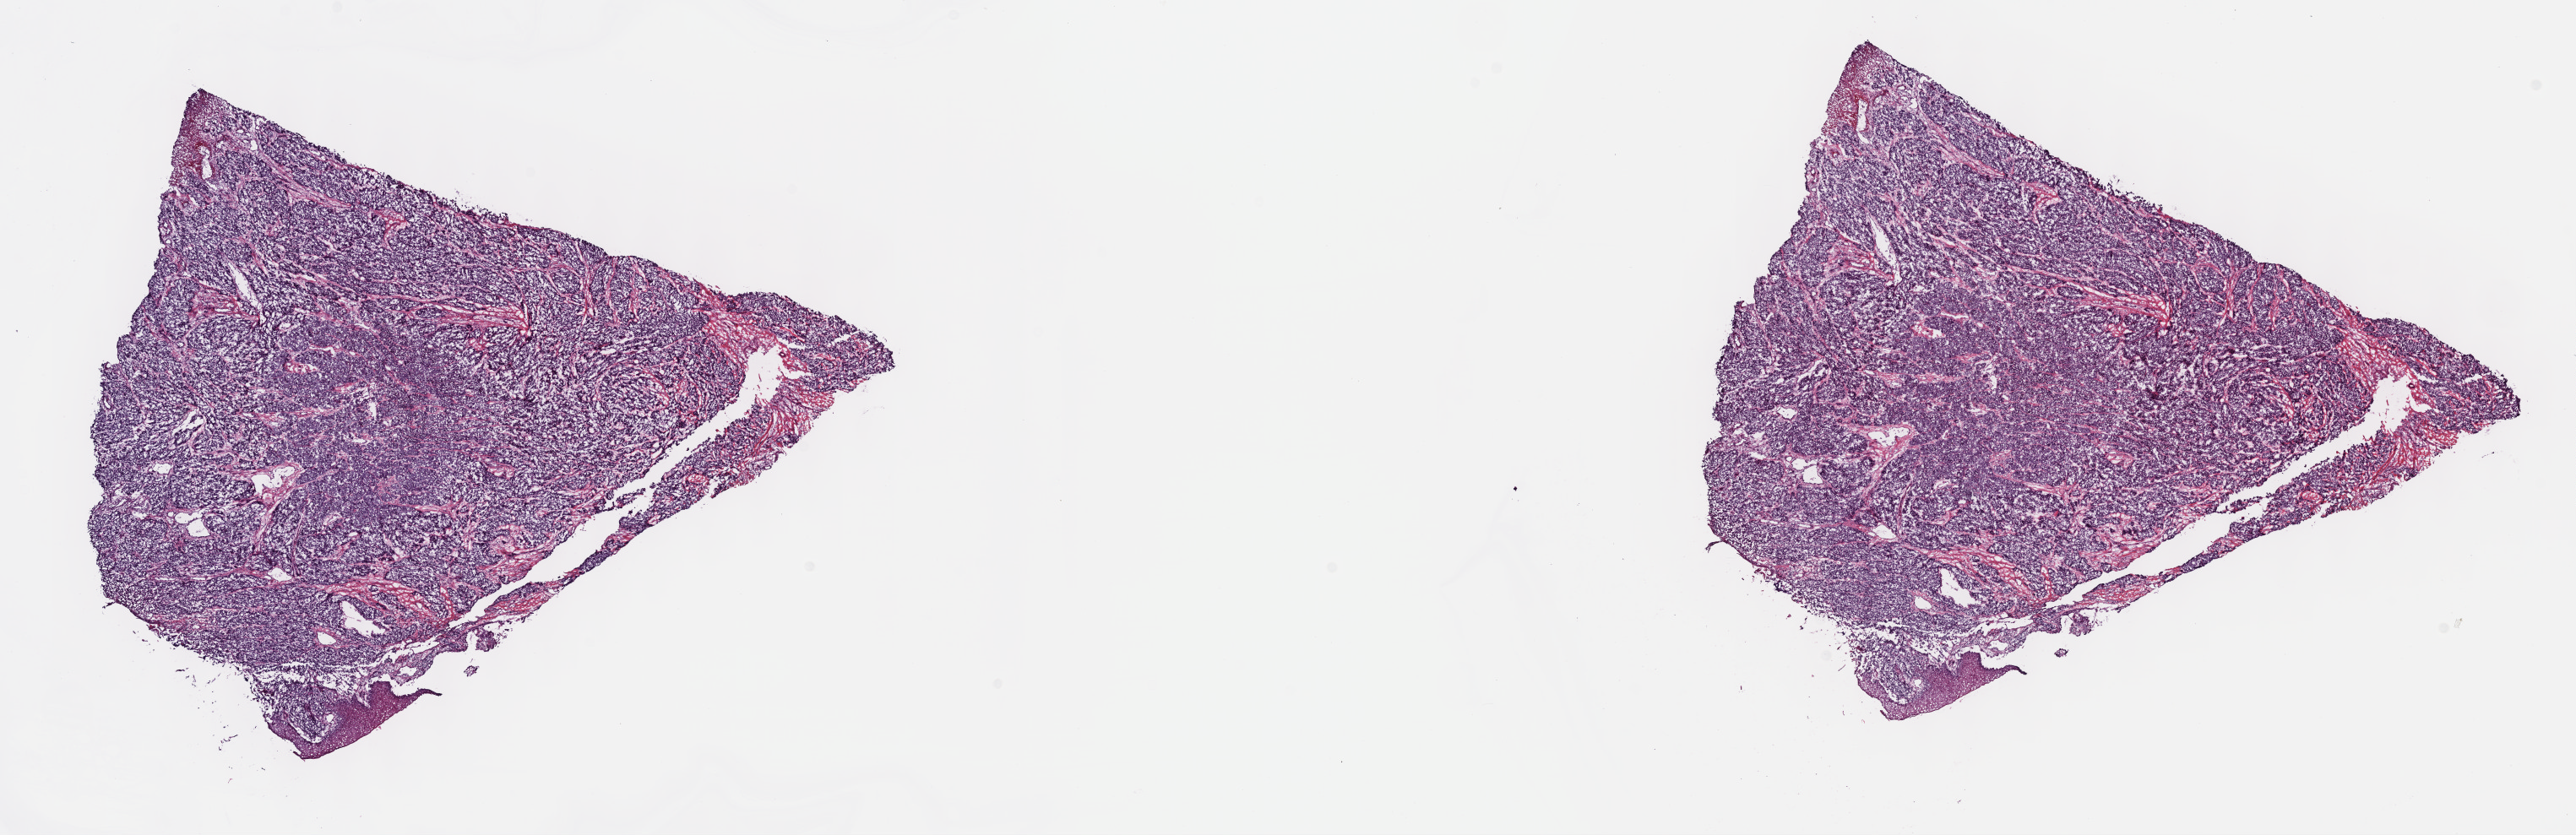
Whole-slide histology image, H&E — low-resolution overview of the scanned area, about 24.7 x 8.0 mm, frozen section from the top of the tissue portion, skin, primary tumour sample. Female, age 70 years at initial diagnosis. Pathologist review of this section (percent, as recorded): tumour cells 100%, tumour nuclei 80%, normal cells 0%, stromal cells 0%, necrosis 0%. Infiltration values recorded for this section: lymphocyte infiltration 2%, monocyte infiltration 0%, neutrophil infiltration 0%.
• pathologic diagnosis: Malignant melanoma, NOS